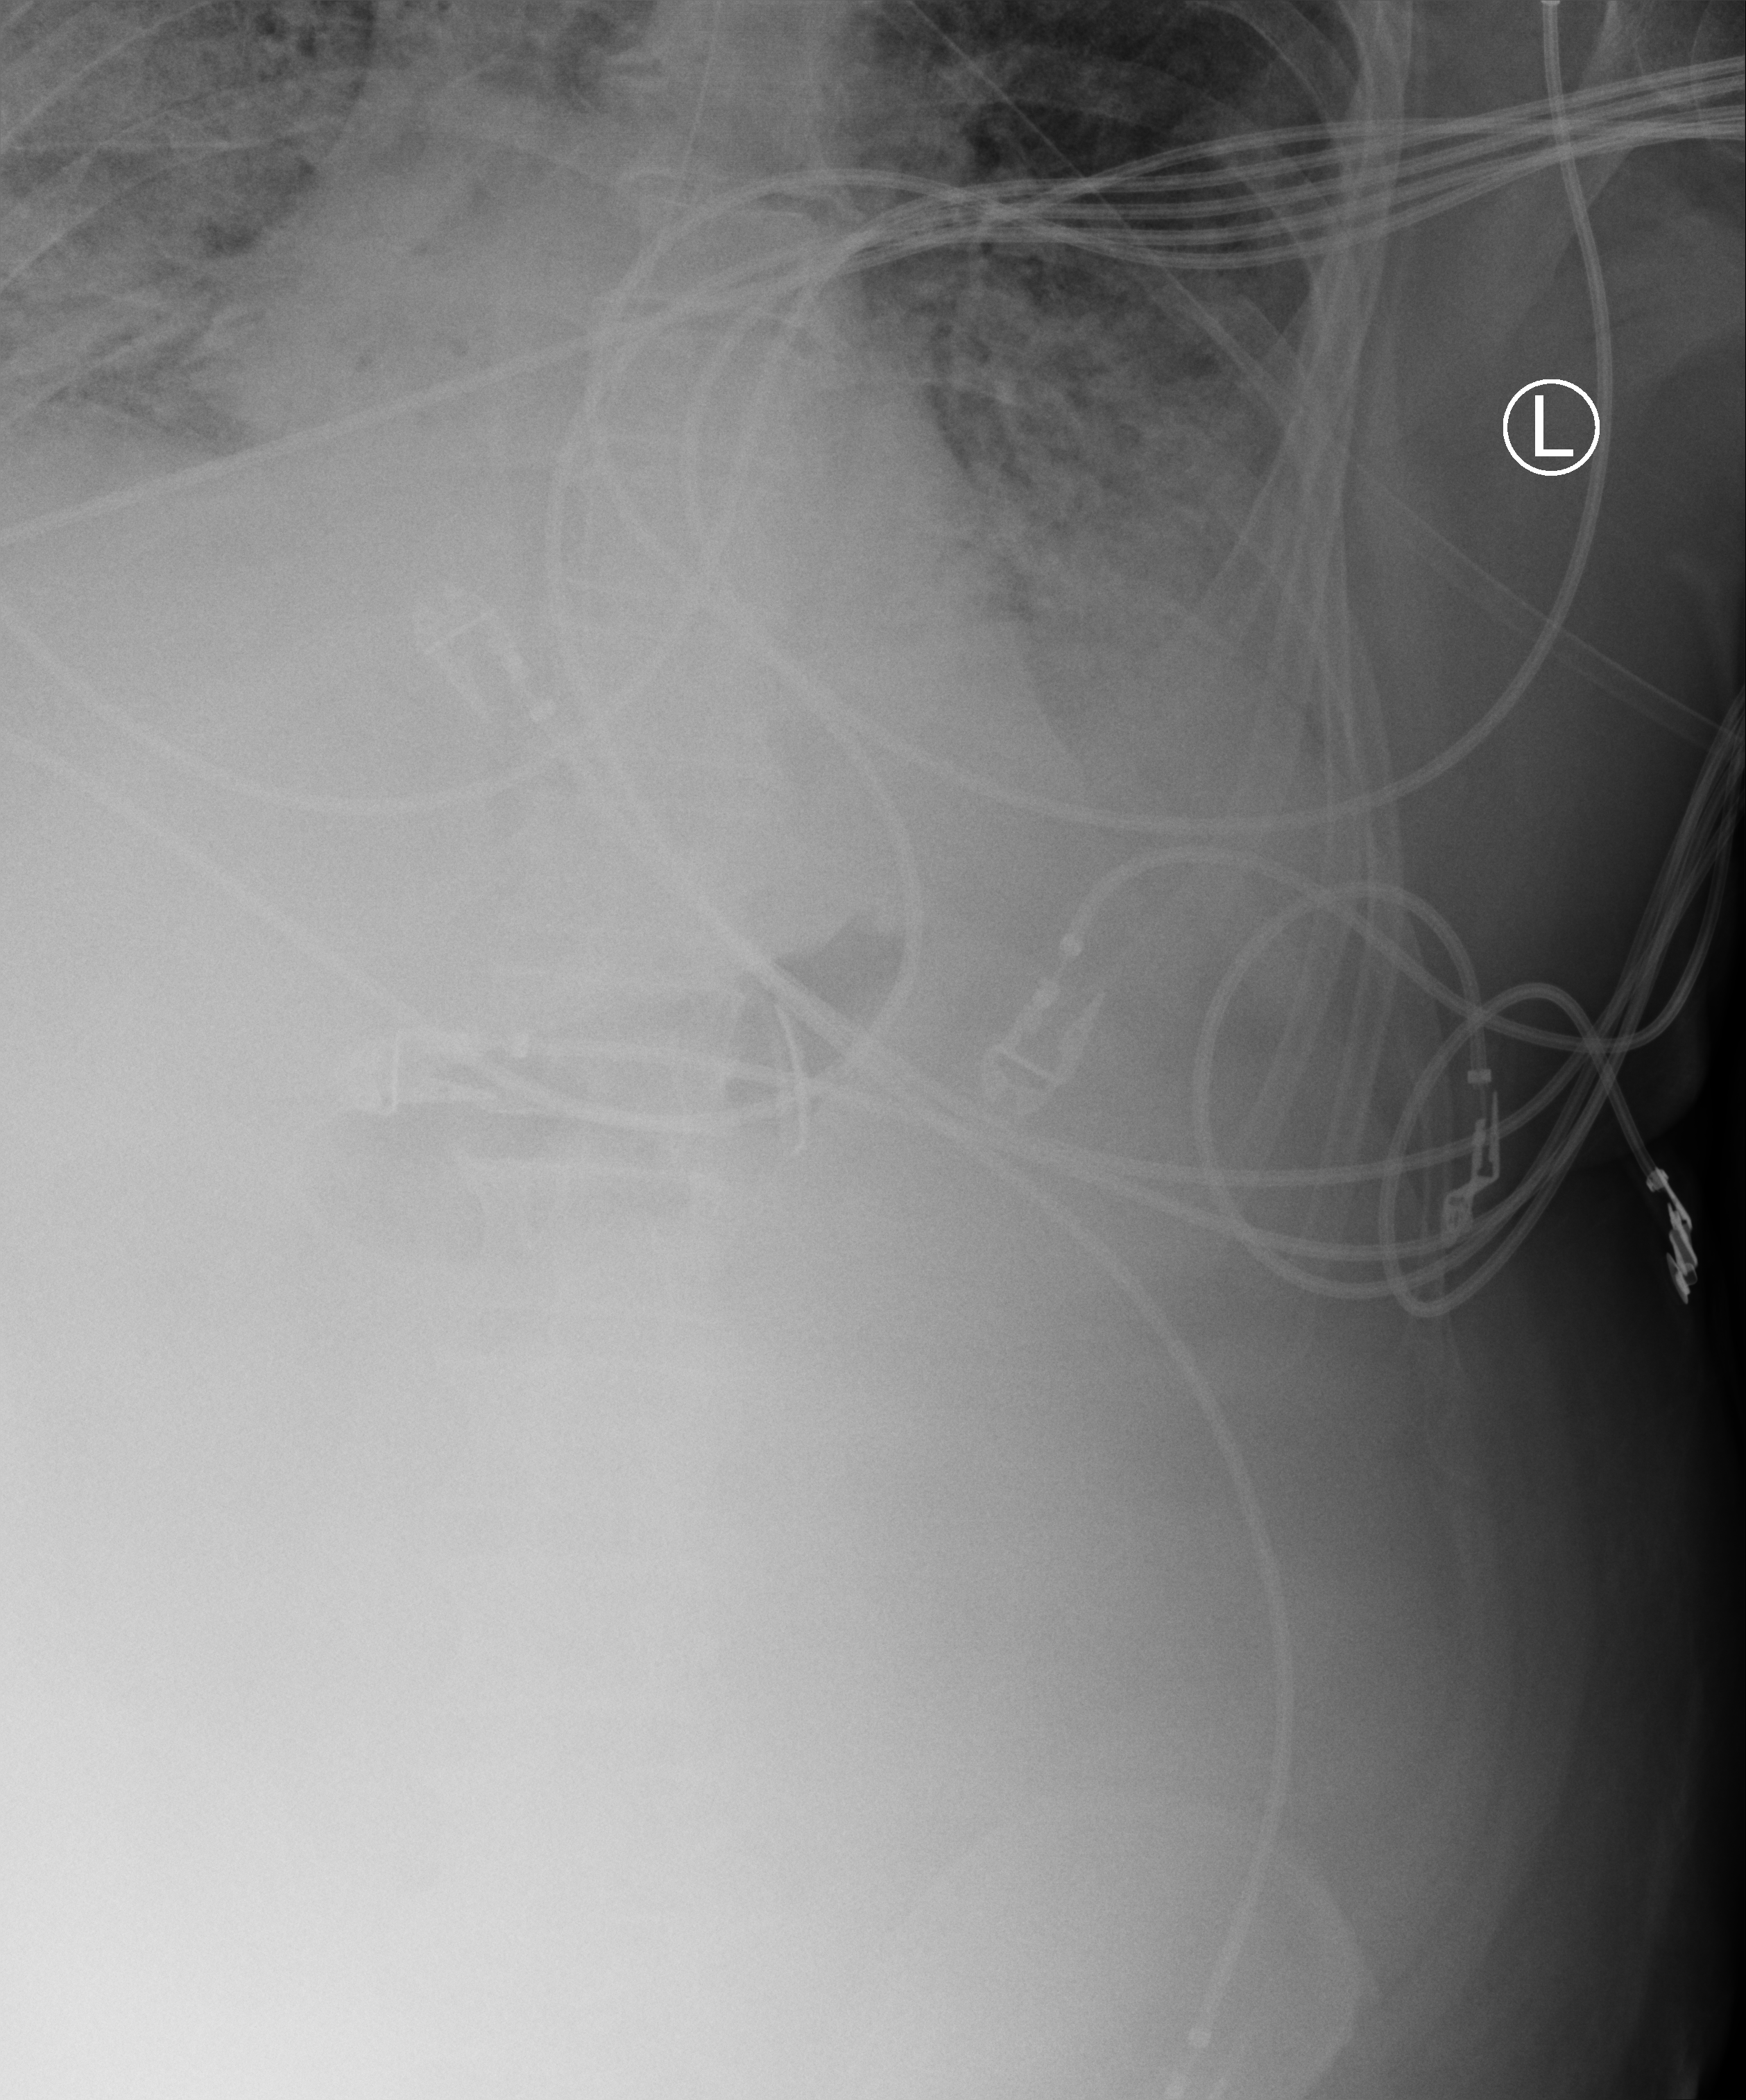
Portable chest radiograph, anteroposterior (AP) projection. Patient hospitalised with COVID-19; male, aged 60–74 years.
From the hospital-stay record, not from the radiograph (when in the stay this image was taken is not recorded):
- mechanically ventilated during this hospital stay: yes
- chronic kidney disease (admission record): no